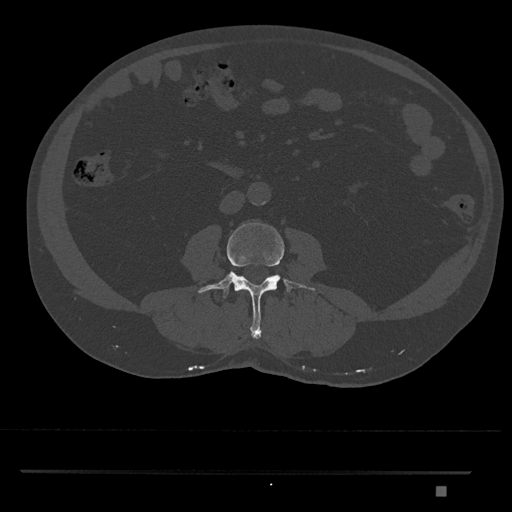
CT including the spine, one axial slice. Position 678 of 1134 along the scan axis. Bone window (W 1800 / L 400 HU). 512 × 512 image matrix, field of view 429 × 429 mm. Male patient, age 65 years. From the clinical record (not read from this slice): primary cancer: prostate.
Structures marked on this image (semi-automatic segmentation, software-assisted and operator-edited):
- L3 vertebra: bounding box [x1, y1, x2, y2] px = [197, 222, 316, 339]